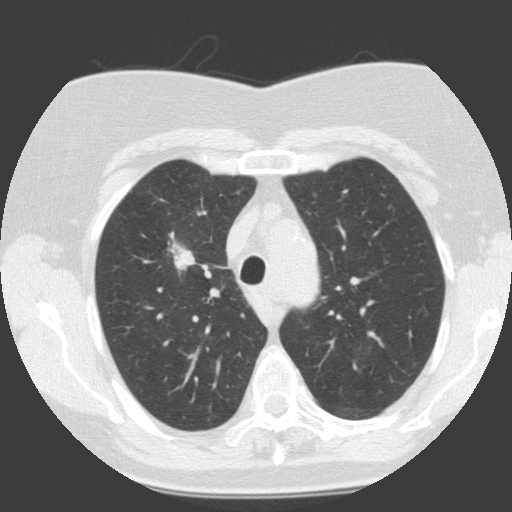
Low-dose screening chest CT, one axial slice; position 106 of 146 along the scan axis; lung window (W 1500 / L -600 HU); 2 mm slice thickness; 512 × 512 image matrix, field of view 300 × 300 mm.
Annotated regions visible in this slice (expert manual segmentation):
- lesion 1 (tumor, upper lobe of right lung): bounding box <167,241,195,273> (left, top, right, bottom; pixels)